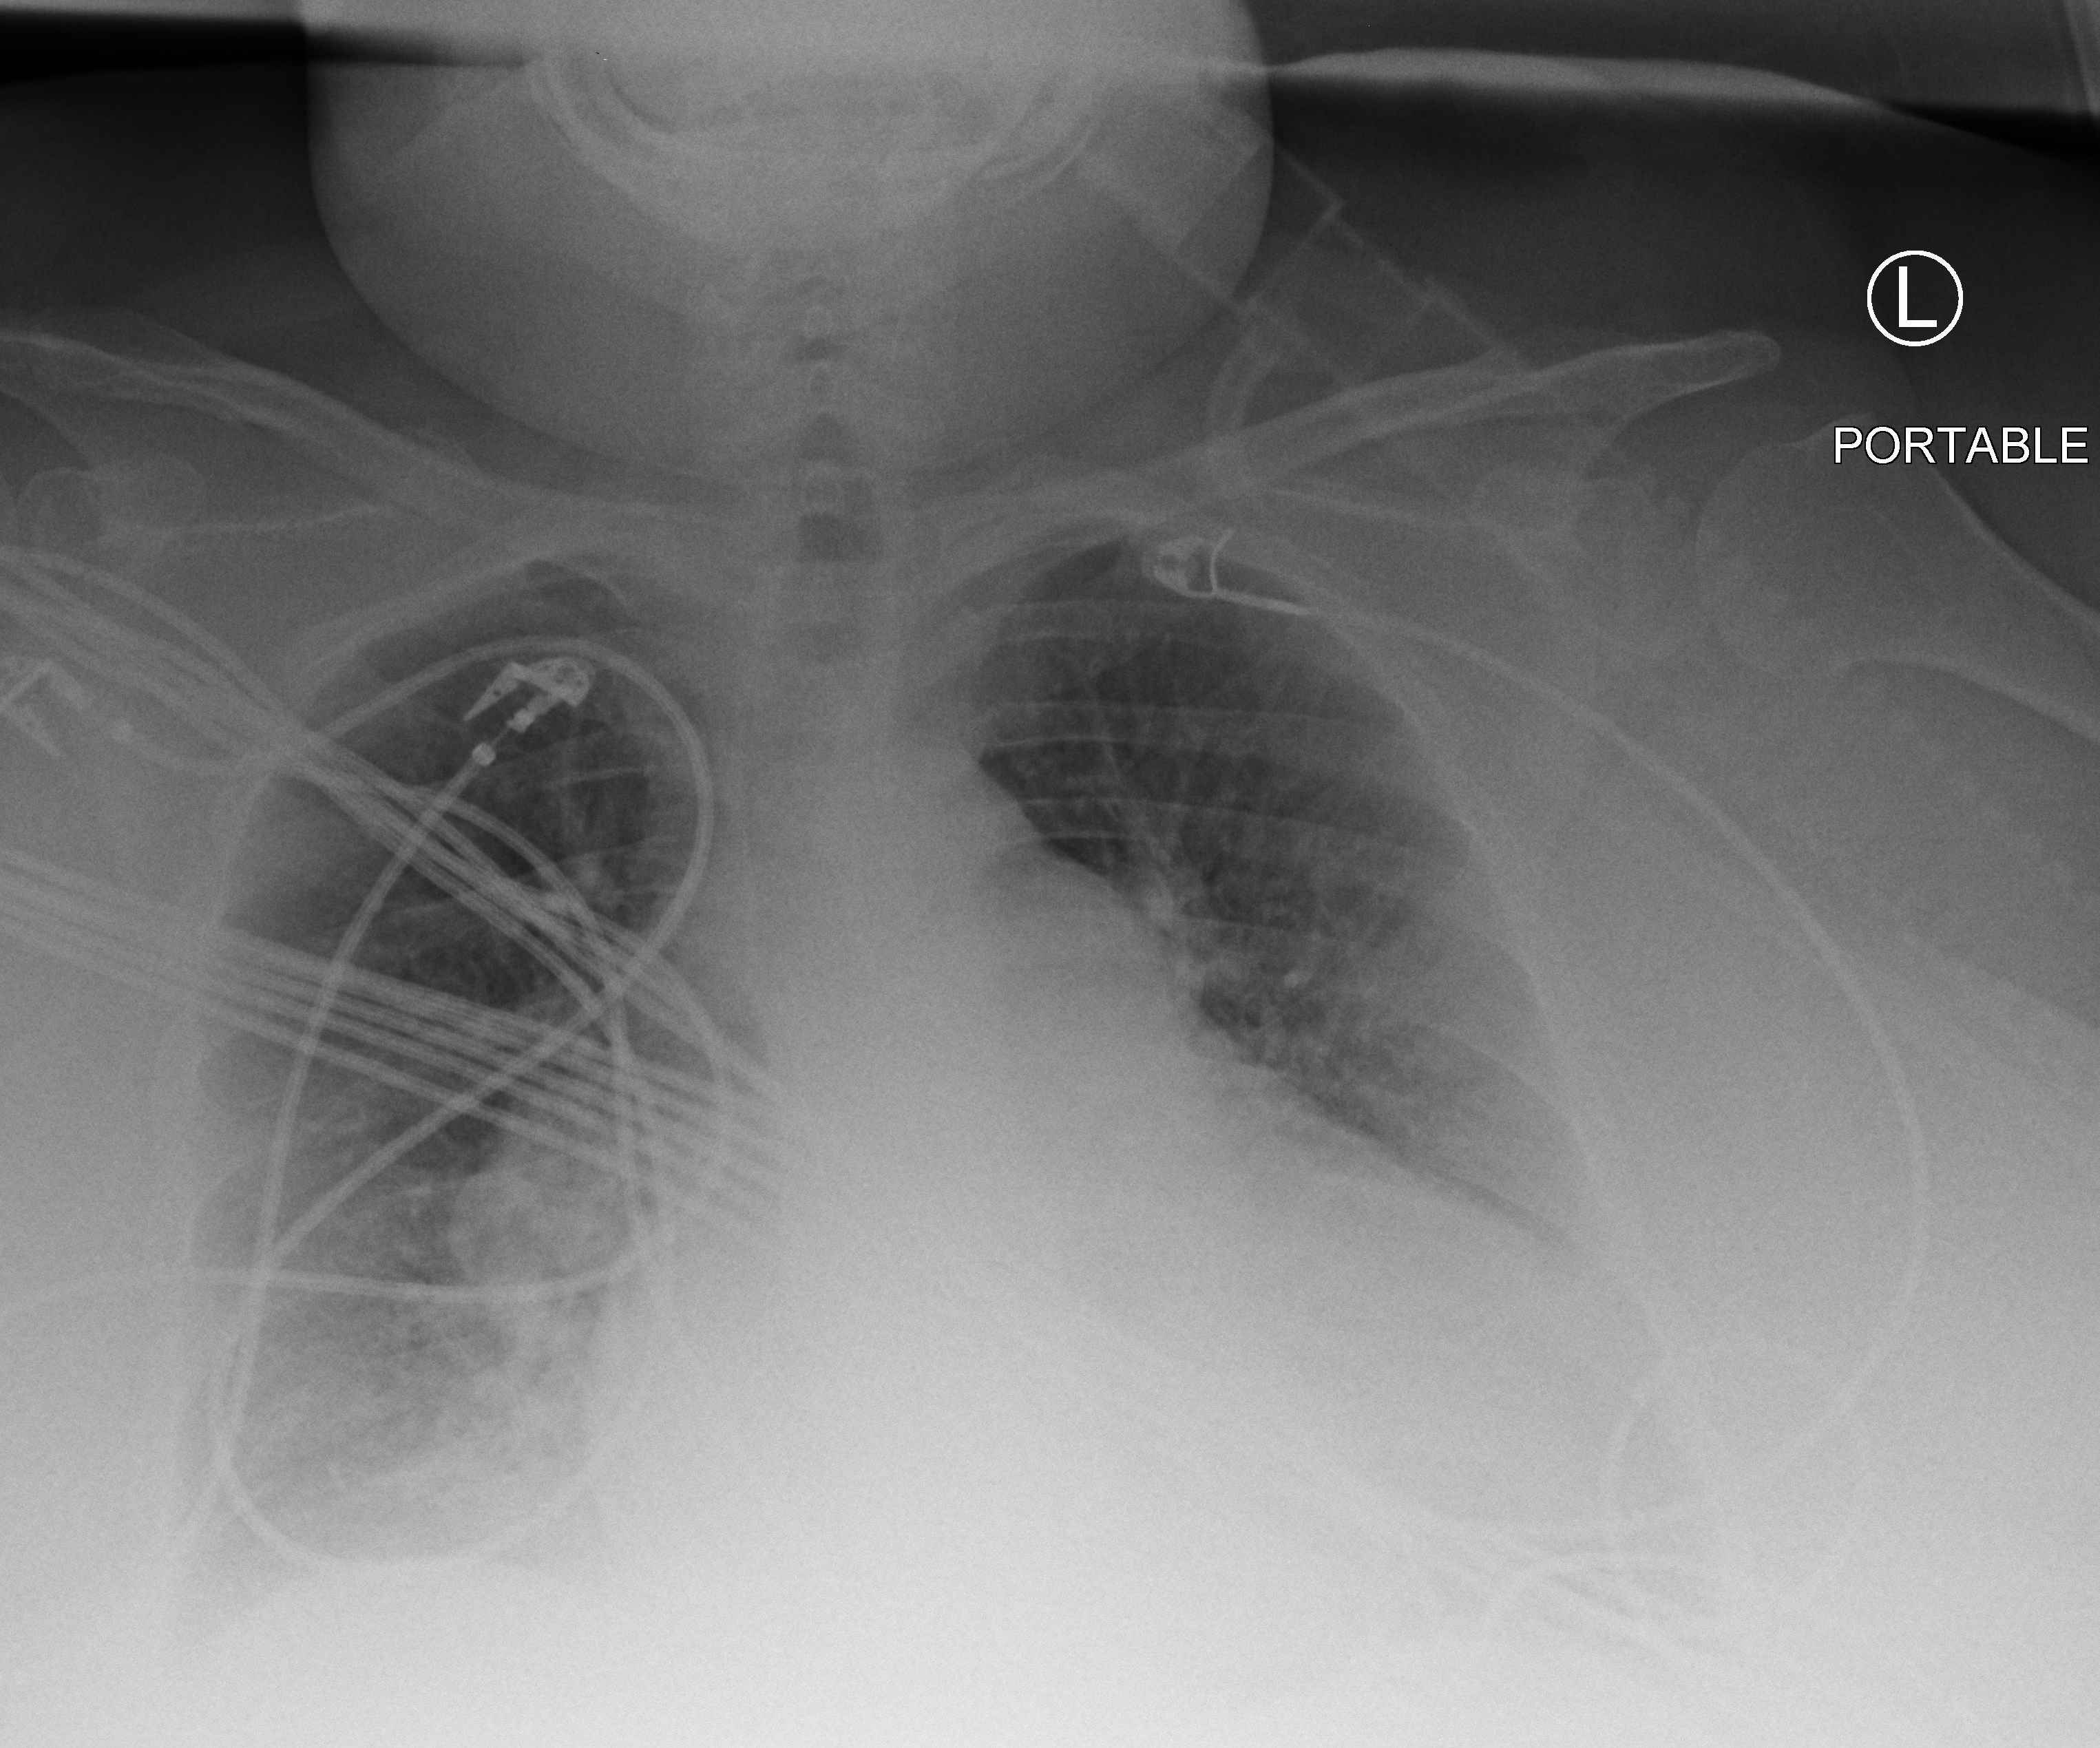
Chest X-ray (portable), anteroposterior (AP) projection. Patient hospitalised with COVID-19; female, aged 60–74 years.
From the hospital-stay record, not from the radiograph (when in the stay this image was taken is not recorded): hypertension (admission record): yes; mechanically ventilated during this hospital stay: yes.